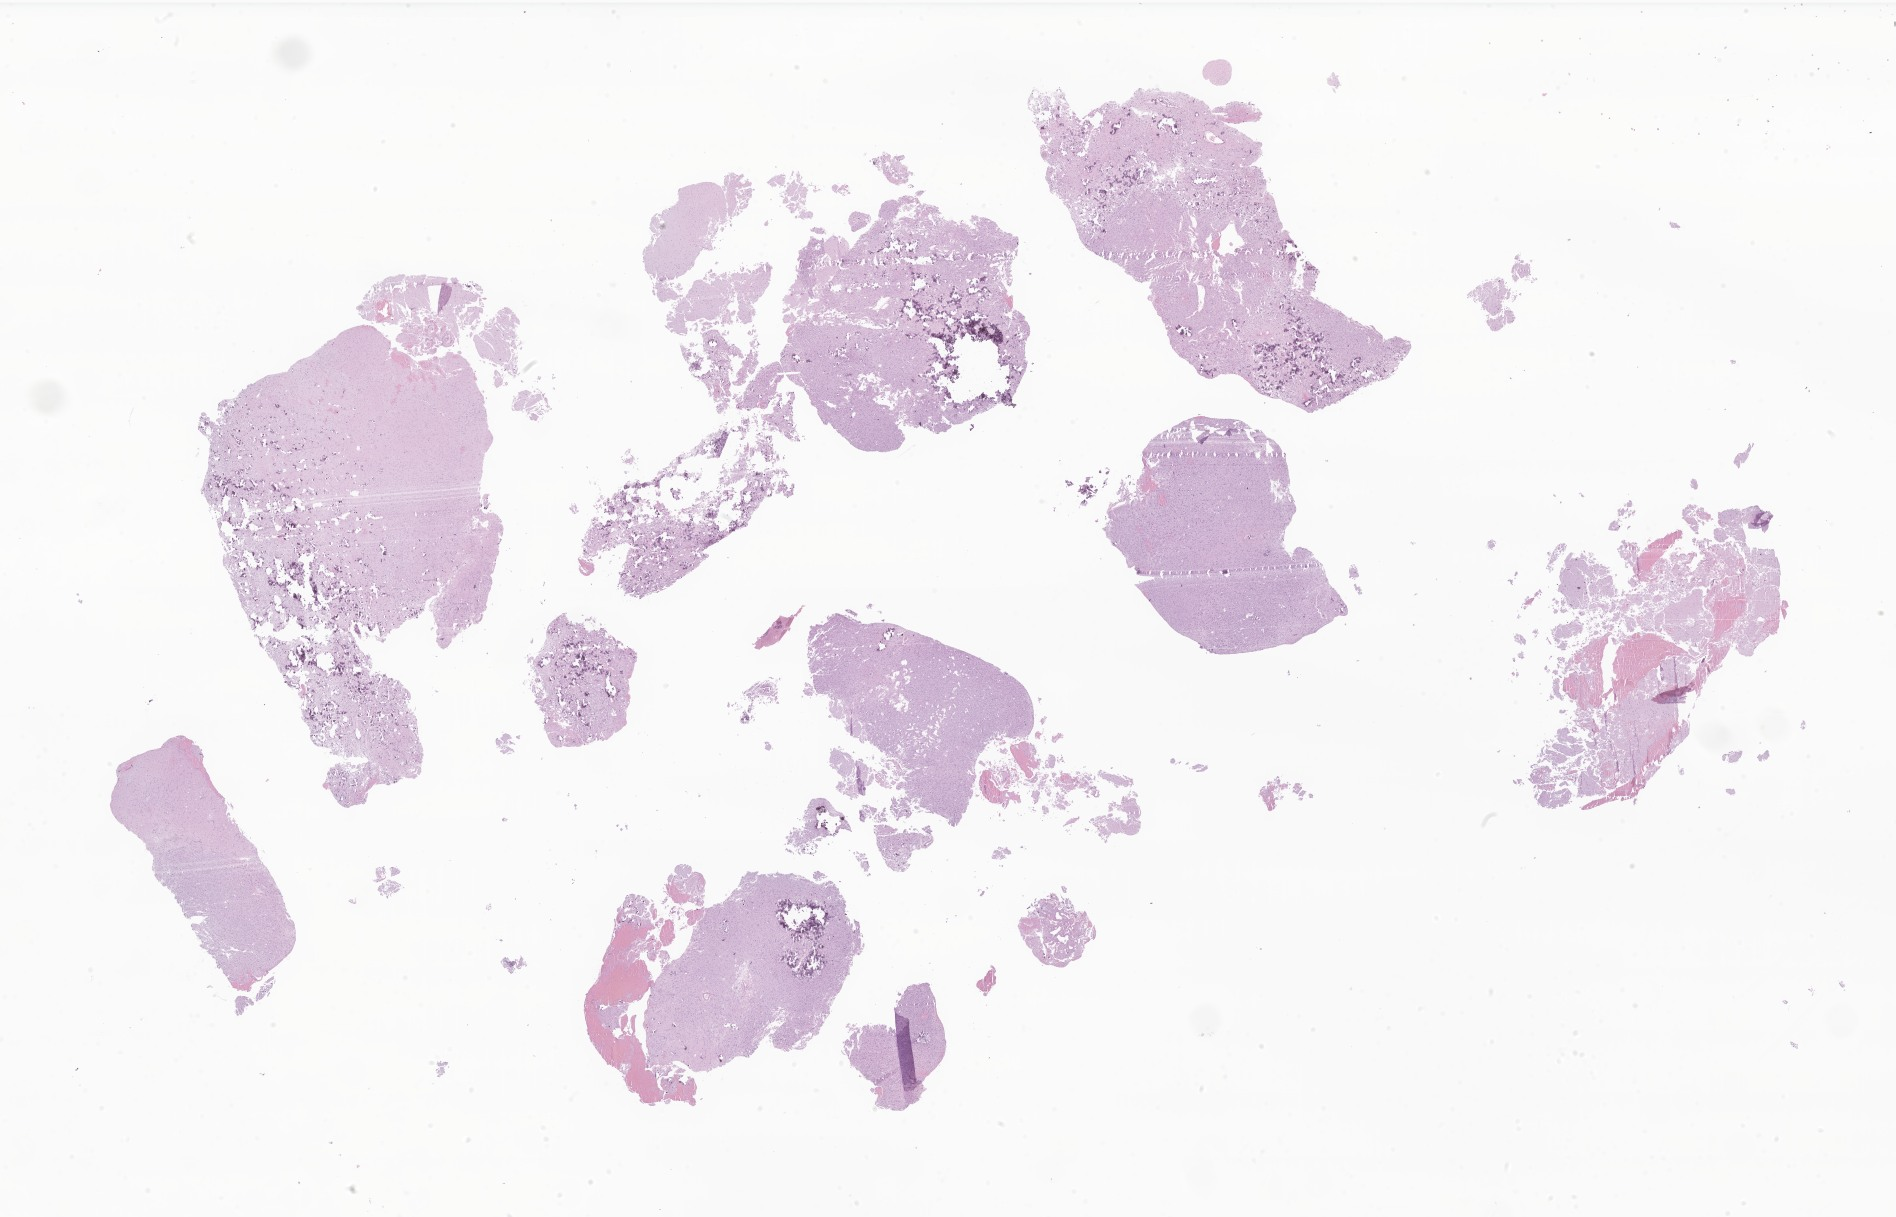
Hematoxylin and eosin (H&E) whole-slide image of tumor tissue from the temporal lobe — shown as a low-resolution overview of the whole scanned area (about 32.0 x 20.5 mm); formalin-fixed, paraffin-embedded (FFPE) tissue. Patient female; age 120 months (10 years).
* recorded diagnosis: Oligoastrocytoma, NOS